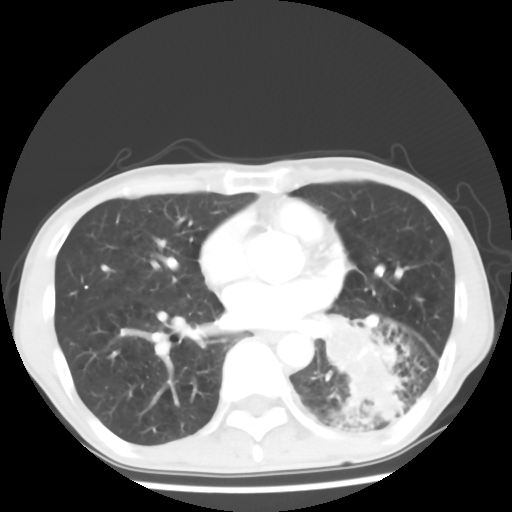
Chest CT, one axial slice. Position 28 of 64 along the scan axis. 120 kVp. Lung window (W 1500 / L -600 HU). 5 mm slice thickness. 512 × 512 image matrix, field of view 313 × 313 mm. Patient: male, 68 years. Case-level facts recorded for this patient, not image findings: clinical TNM (as recorded): T4 N0 M0.
Outlined on this slice (rectangle marked by the reading radiologist):
- lung tumour (recorded histology: squamous cell carcinoma): bounding box (x1, y1, x2, y2) in pixels: (317, 301, 416, 429)